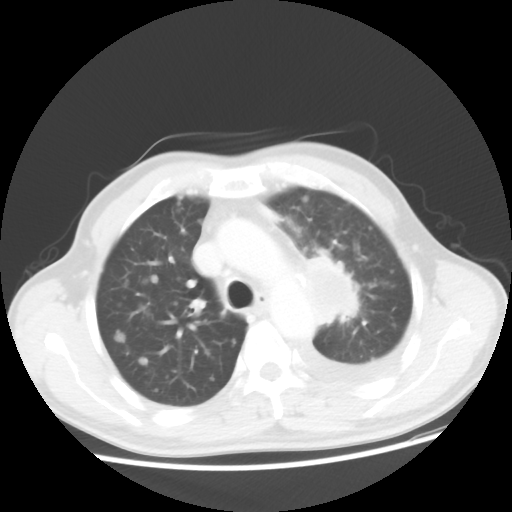
Chest CT, one axial slice; slice 34 of 48 in the series (ordered by position); reconstruction kernel STANDARD; 100 kVp; lung window (W 1500 / L -600 HU); 5 mm slice thickness; 512 × 512 image matrix. Patient: male, 55 years. From the clinical record (not read from this slice): clinical TNM (as recorded): T2 N3 M1a.
Outlined on this slice (bounding box drawn by a radiologist):
- lung tumour (recorded histology: squamous cell carcinoma): bounding box [x1, y1, x2, y2] px = [292, 250, 369, 339]